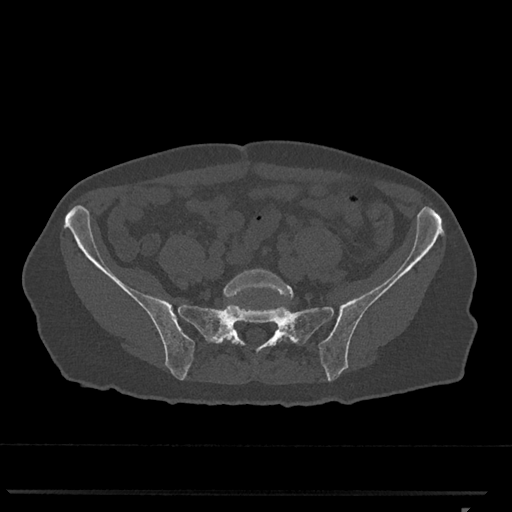
CT including the spine, one axial slice. Position 116 of 793 along the scan axis. 120 kVp. Bone window (W 1800 / L 400 HU). 0.5 mm slice thickness. 512 × 512 image matrix, field of view 380 × 380 mm. Female patient, age 62 years. Case-level facts recorded for this patient, not image findings: primary cancer: renal.
Outlined on this slice (semi-automatic segmentation, software-assisted and operator-edited):
- L5 vertebra: bounding box [x1, y1, x2, y2] px = [223, 269, 295, 341]